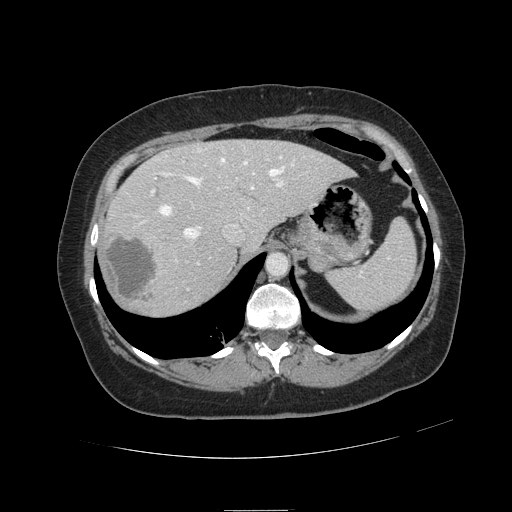
Contrast-enhanced abdominal CT, one axial slice; 120 kVp; intravenous contrast given; soft-tissue window (W 400 / L 40 HU); 2.5 mm slice thickness; 512 × 512 image matrix, field of view 400 × 400 mm. Female patient, age 52 years. From the clinical record (not read from this slice): diagnosis: colorectal cancer liver metastases, imaged before liver resection; multiple liver metastases: yes; largest metastasis: 6.3 cm; chemotherapy before resection: yes.
Outlined on this slice (expert manual segmentation):
- hepatic veins: bounding box [x1, y1, x2, y2] px = [160, 150, 293, 238]
- liver: [103, 140, 351, 315]
- planned liver remnant (the part of the liver to remain after resection): [168, 140, 351, 248]
- portal vein (with intrahepatic branches): [151, 159, 284, 290]
- liver metastasis: [105, 235, 156, 304]